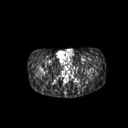
FDG PET of an extremity soft-tissue mass (from a PET/CT study), one axial slice; position 46 of 267 along the scan axis; 3.27 mm slice thickness; 128 × 128 image matrix, field of view 600 × 600 mm. Male patient, age 59 years. From the clinical record (not read from this slice): histological type: pleiomorphic liposarcoma; grade: high; site of the primary tumour: left thigh.
Outlined on this slice (expert contour drawn on MRI and transferred to this co-registered scan by the dataset authors):
- gross tumour volume including surrounding oedema: bounding box (x1, y1, x2, y2) in pixels: (70, 69, 77, 75)